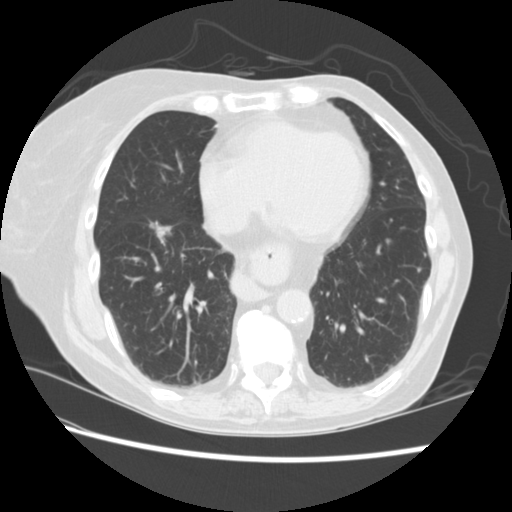
Low-dose screening chest CT, one axial slice; slice 74 of 224 in the series (ordered by position); reconstruction kernel STANDARD; lung window (W 1500 / L -600 HU); 2.5 mm slice thickness; 512 × 512 image matrix, field of view 340 × 340 mm.
Structures marked on this image (outlined manually by an expert reader):
- lesion 2 (tumor, lower lobe of right lung): box from (x=152, y=224) to (x=170, y=240) px